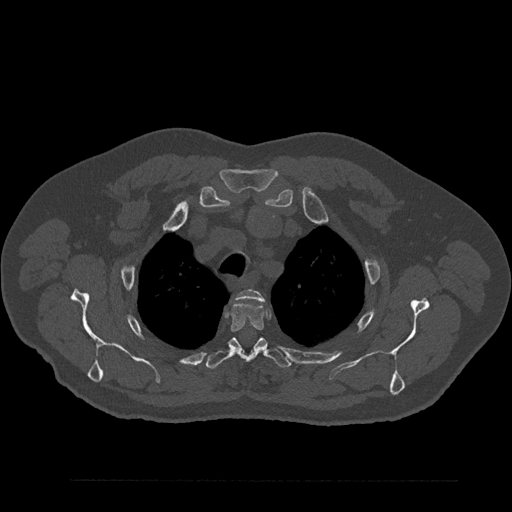
CT including the spine, one axial slice. Position 670 of 797 along the scan axis. 120 kVp. Bone window (W 1800 / L 400 HU). 0.5 mm slice thickness. 512 × 512 image matrix. Patient: male, 61 years. From the clinical record (not read from this slice): primary cancer: prostate.
Structures marked on this image (semi-automatically segmented with operator editing):
- T2 vertebra: bounding box [x1, y1, x2, y2] px = [237, 289, 265, 302]
- T3 vertebra: [230, 302, 264, 332]
- T4 vertebra: [206, 337, 291, 369]